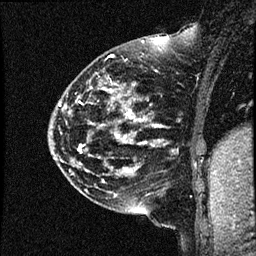
Breast MRI (dynamic contrast-enhanced), one sagittal slice. Slice 14 of 44 in the series (ordered by position). Dynamic contrast-enhanced study with each time point stored as its own series, time point 2 of 4 at this slice position (early post-contrast, ordered by acquisition time). 1.5 T. TE 4.2 ms, TR 17.7 ms. 2 mm slice thickness. 256 × 256 image matrix, field of view 200 × 200 mm. Patient: female, 52 years. Case-level facts recorded for this patient, not image findings: setting: breast cancer imaged before/during neoadjuvant chemotherapy; receptor status: HR-positive, HER2-negative.
Outlined on this slice (semi-automatic segmentation, software-assisted and operator-edited):
- analysis volume of interest (the breast-tissue region the enhancement analysis was run in; not a lesion): box from (x=48, y=48) to (x=163, y=147) px
- tumour enhancement mask (voxels above the 100 % enhancement threshold inside the analysis volume of interest): (x=80, y=111)–(x=132, y=146)